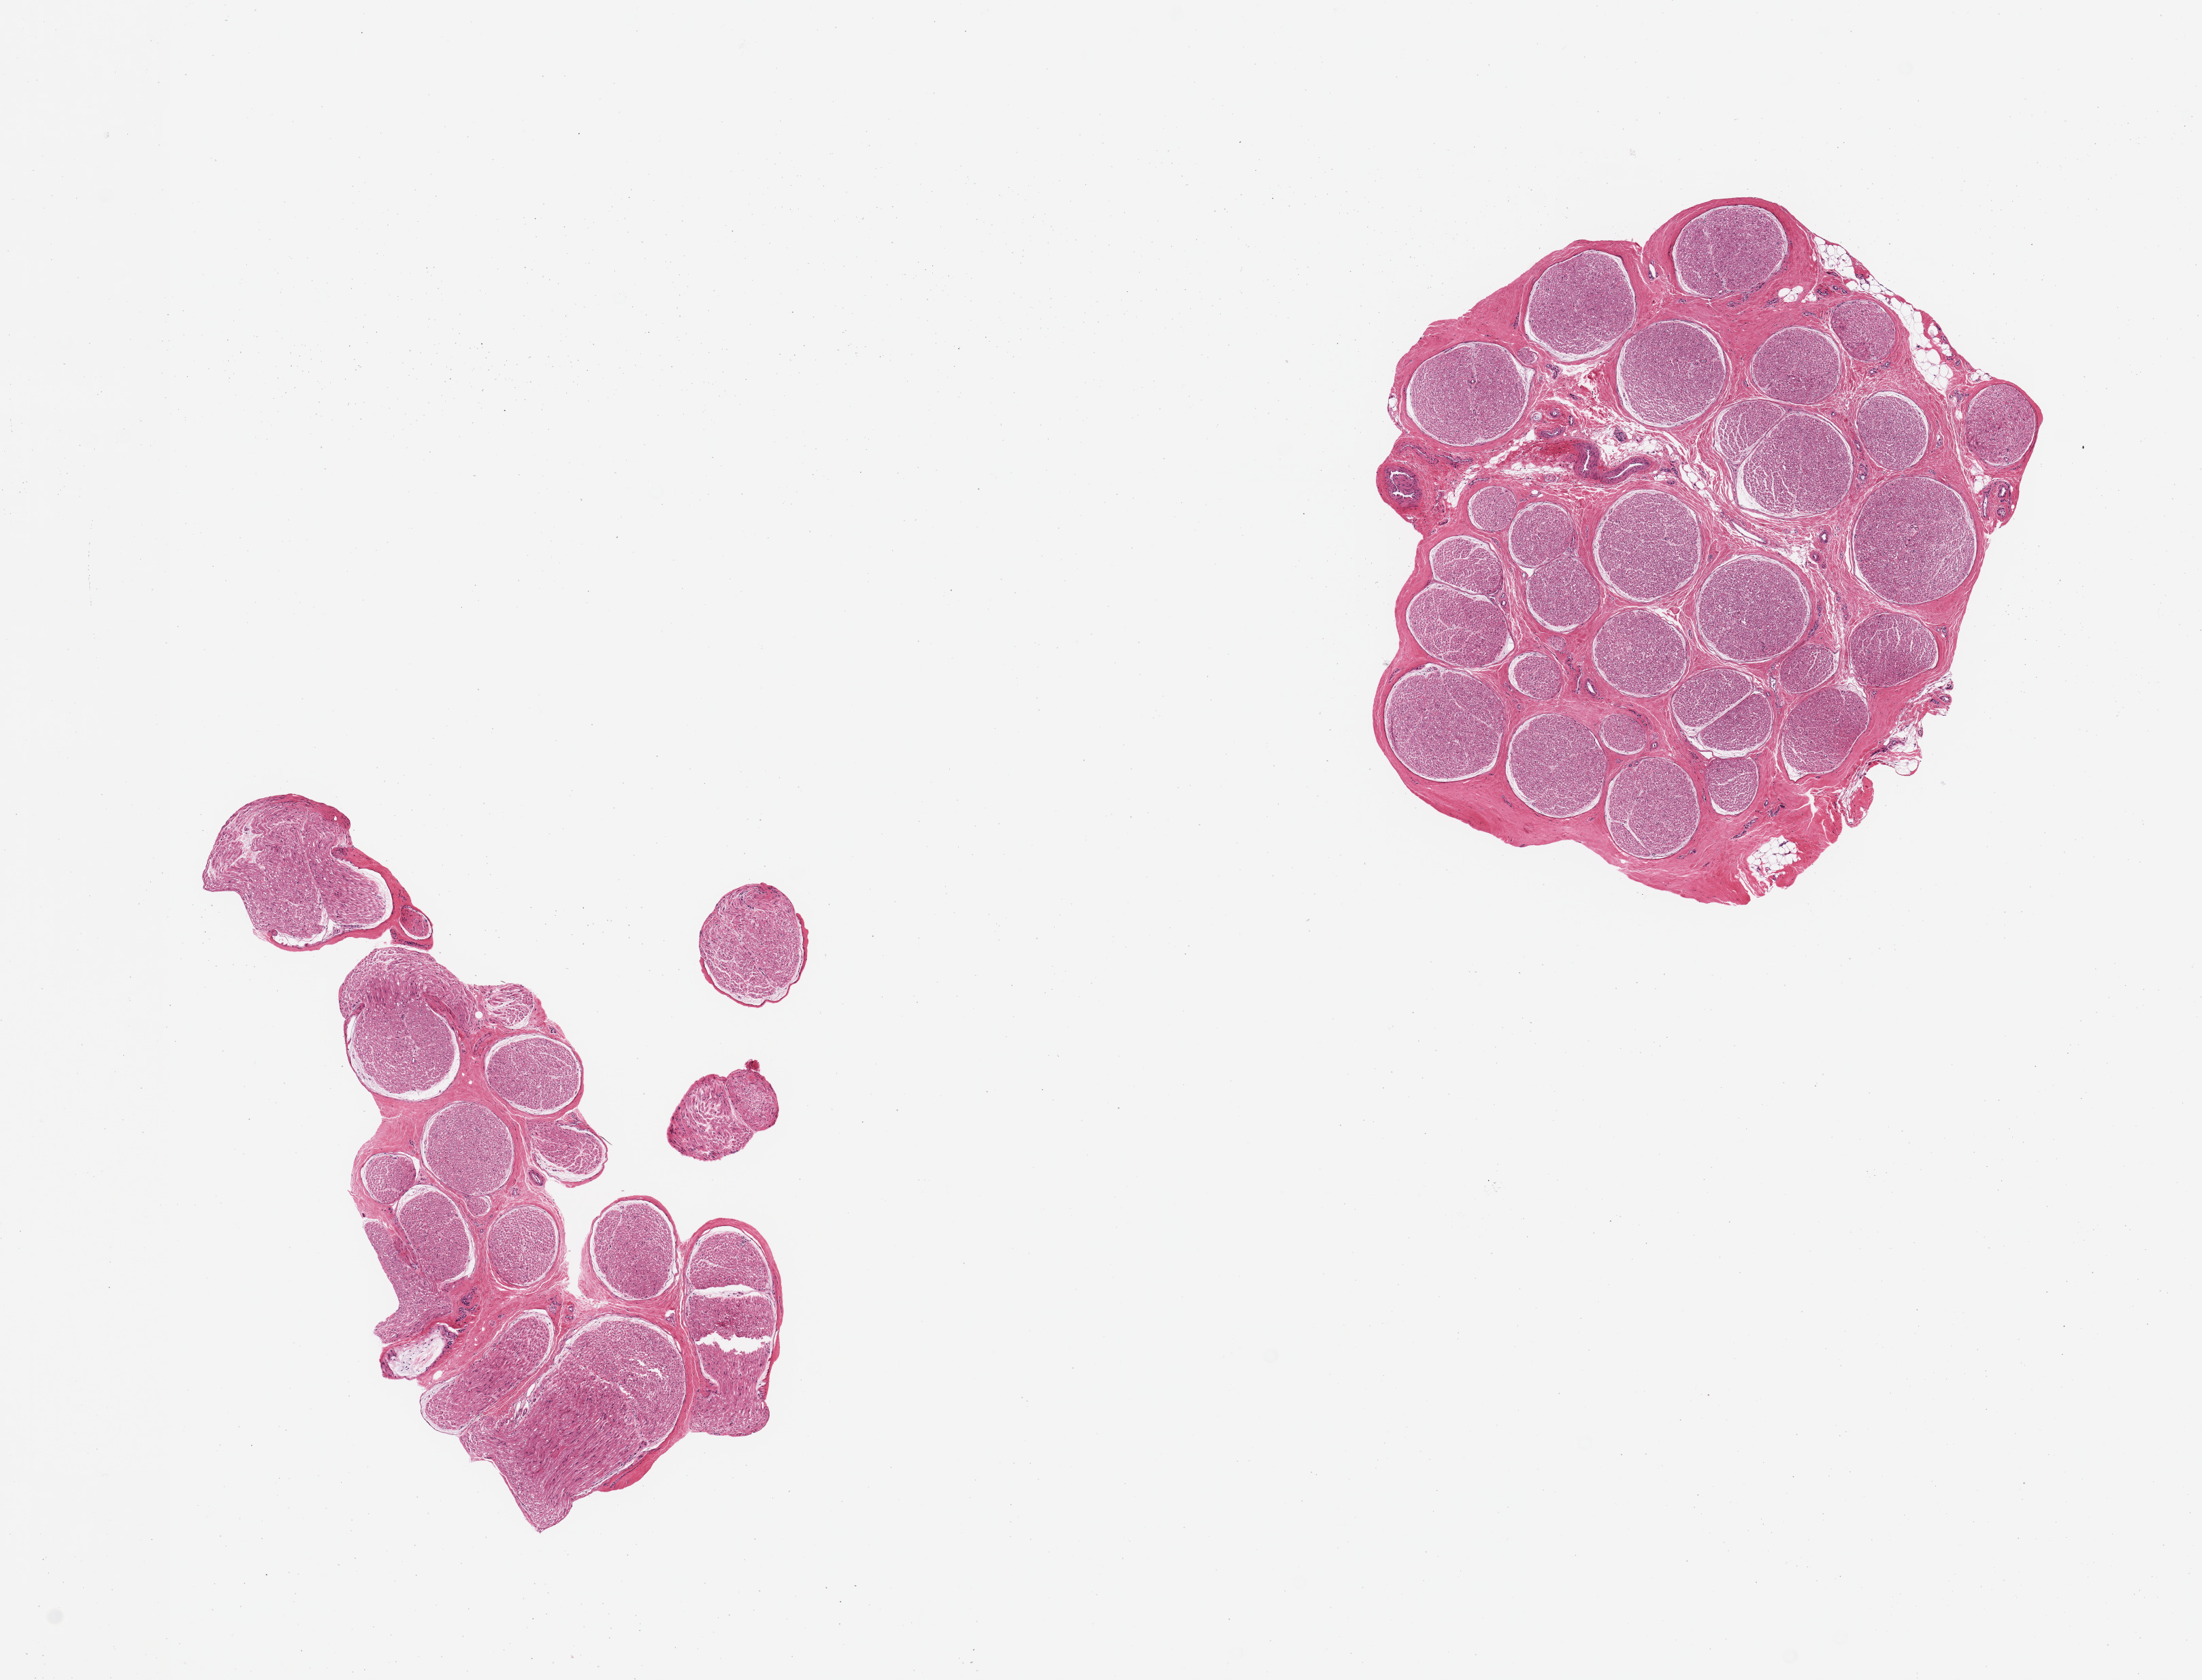
Haematoxylin and eosin whole-slide image — shown as a low-resolution overview of the whole scanned area (about 12.8 x 9.8 mm, slide scanned at 20x), PAXgene-fixed paraffin-embedded (PFPE) section, target tissue: tibial nerve, donor tissue sample. Donor sex: female.
• pathologist's review note for this sample: 2 pieces; nerves with prineurium and trace of external fat